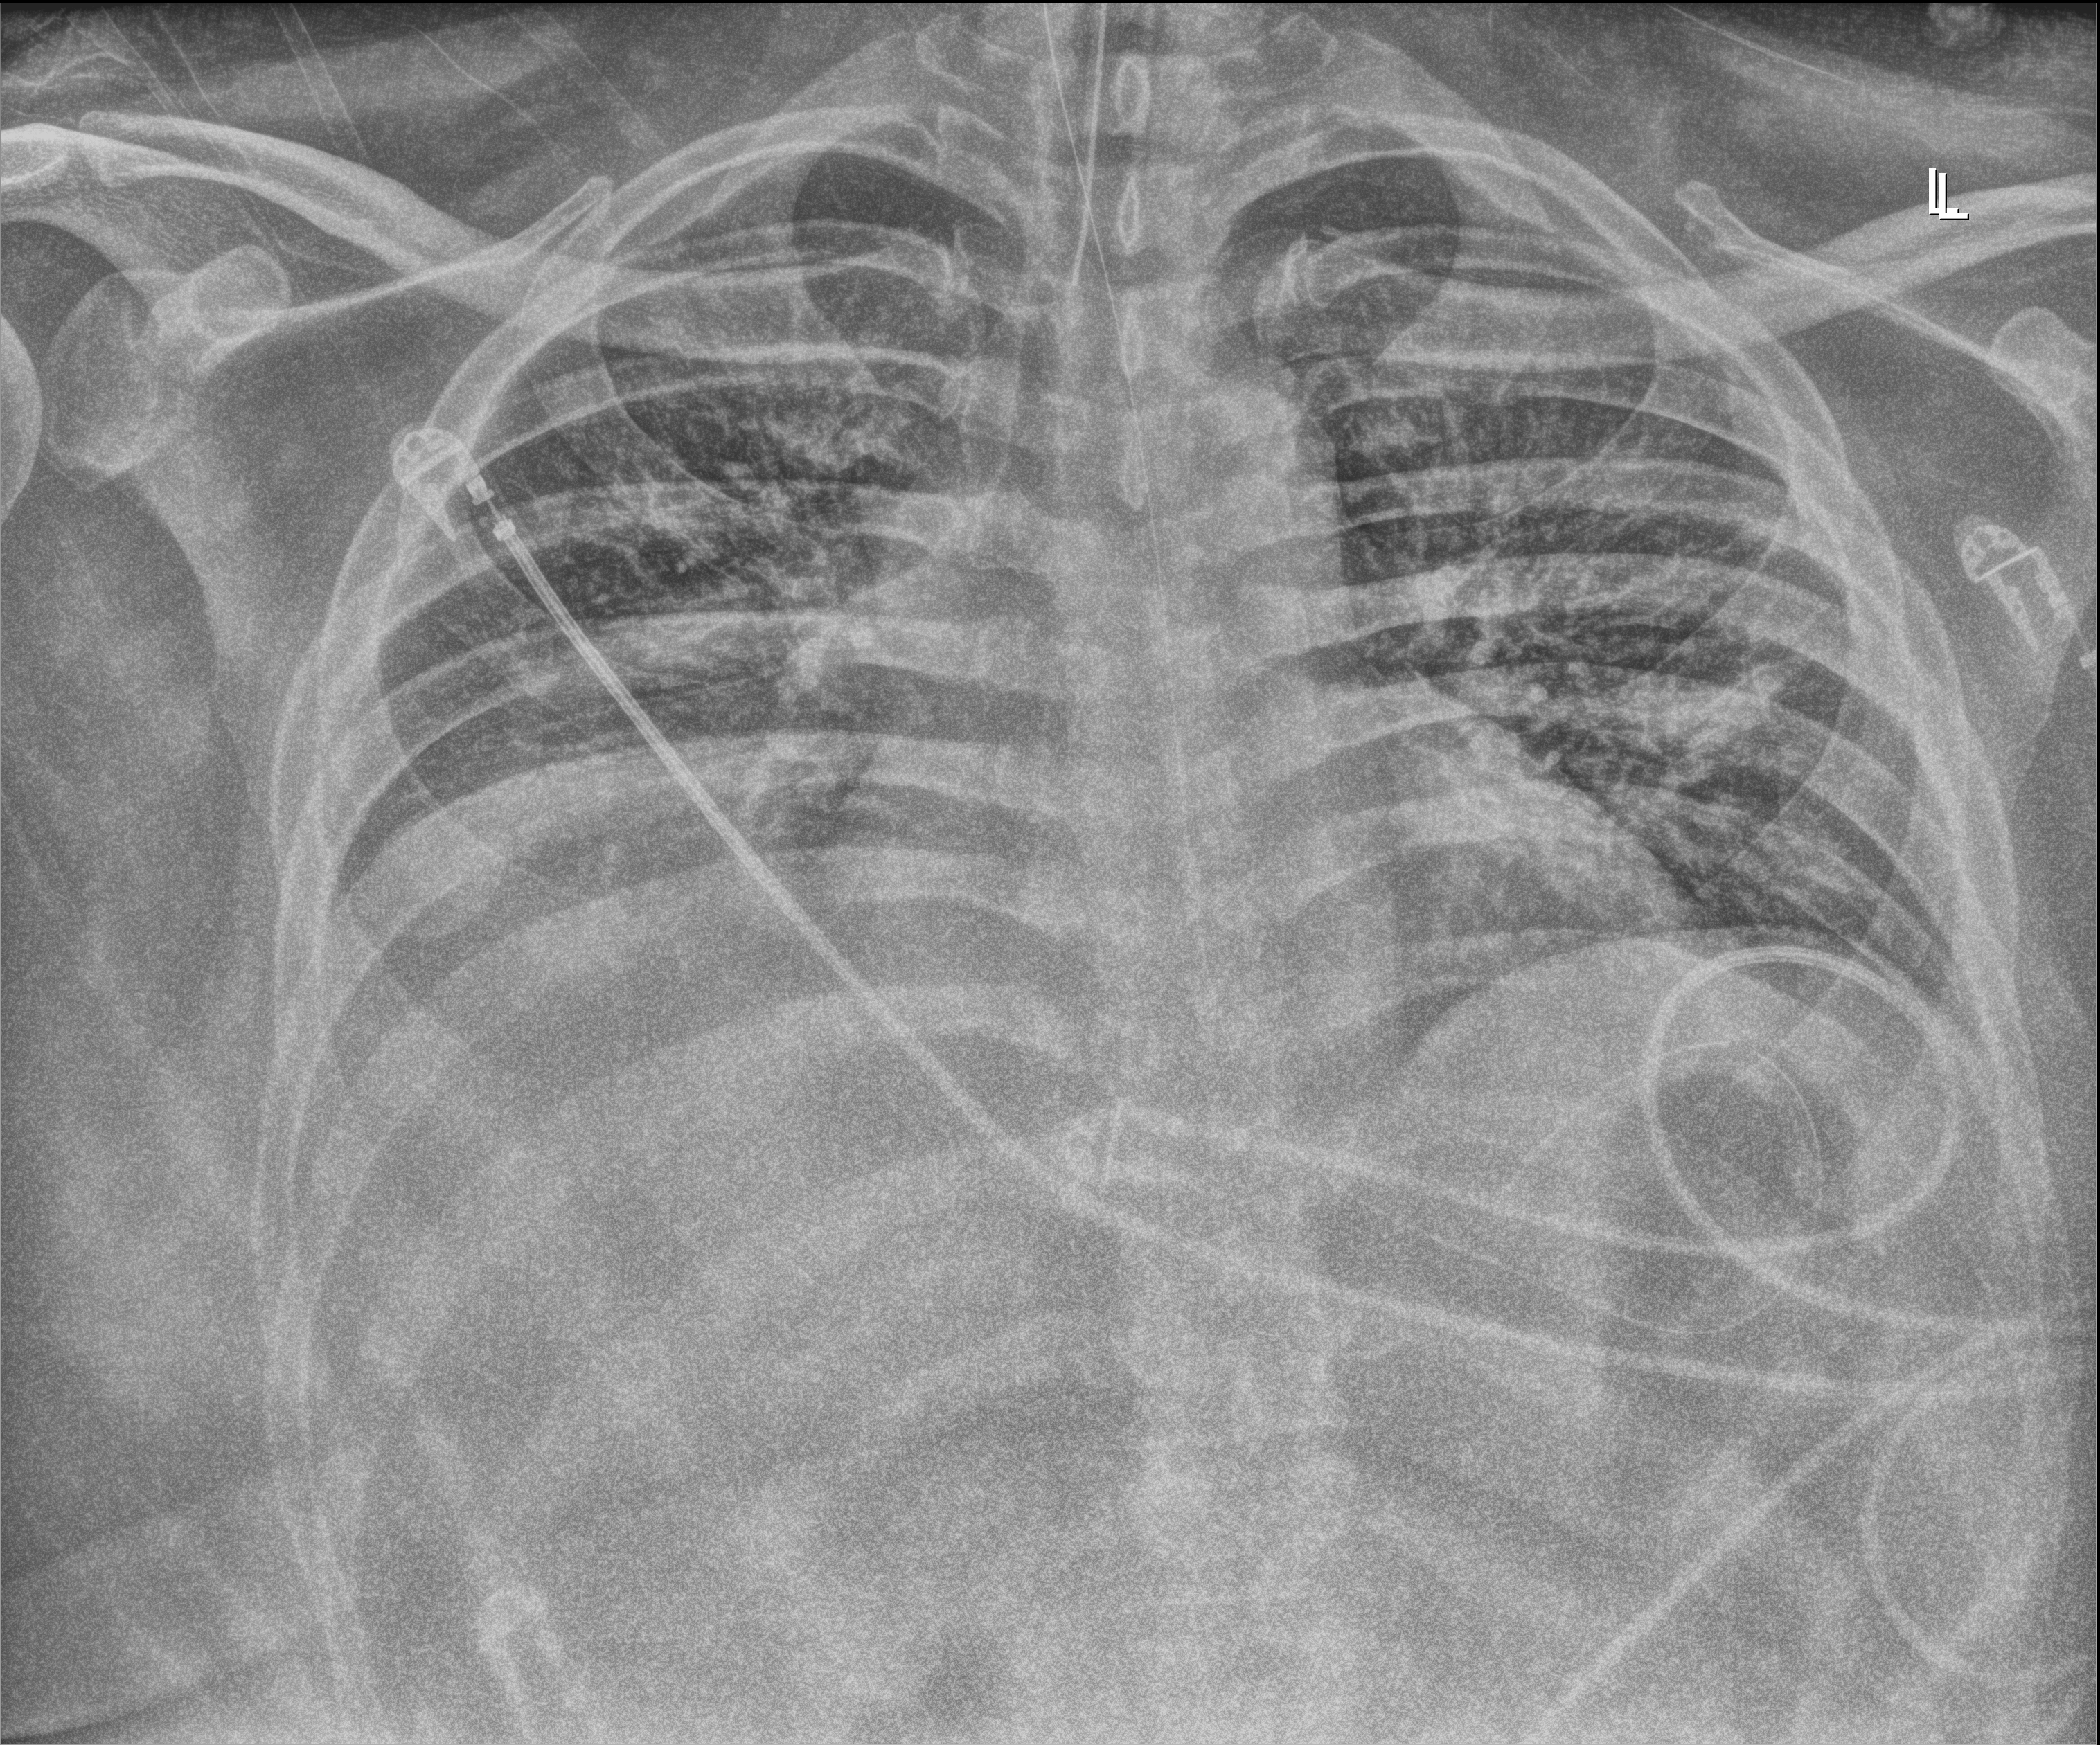
Bedside chest radiograph (digital radiography), anteroposterior (AP) projection. Male patient hospitalised with COVID-19, age 18–59 years.
Hospital-stay facts (about this admission, not read from this image; timing relative to this image not recorded): chronic kidney disease (admission record): no; length of hospital stay: 69 days; other chronic lung disease (admission record): yes.